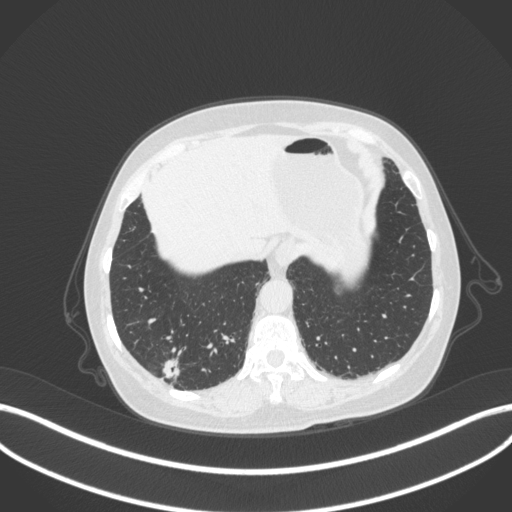
Chest CT, one axial slice. Slice 53 of 340 in the series (ordered by position). Reconstruction kernel B31f. 120 kVp. Lung window (W 1500 / L -600 HU). 1 mm slice thickness. 512 × 512 image matrix, field of view 400 × 400 mm. Patient: female, 69 years. Case-level facts recorded for this patient, not image findings: clinical TNM (as recorded): T1b N0 M0; histopathological grade: G2-3.
Annotated regions visible in this slice (rectangle marked by the reading radiologist):
- lung tumour (recorded histology: adenocarcinoma): bounding box <158,354,183,383> (left, top, right, bottom; pixels)